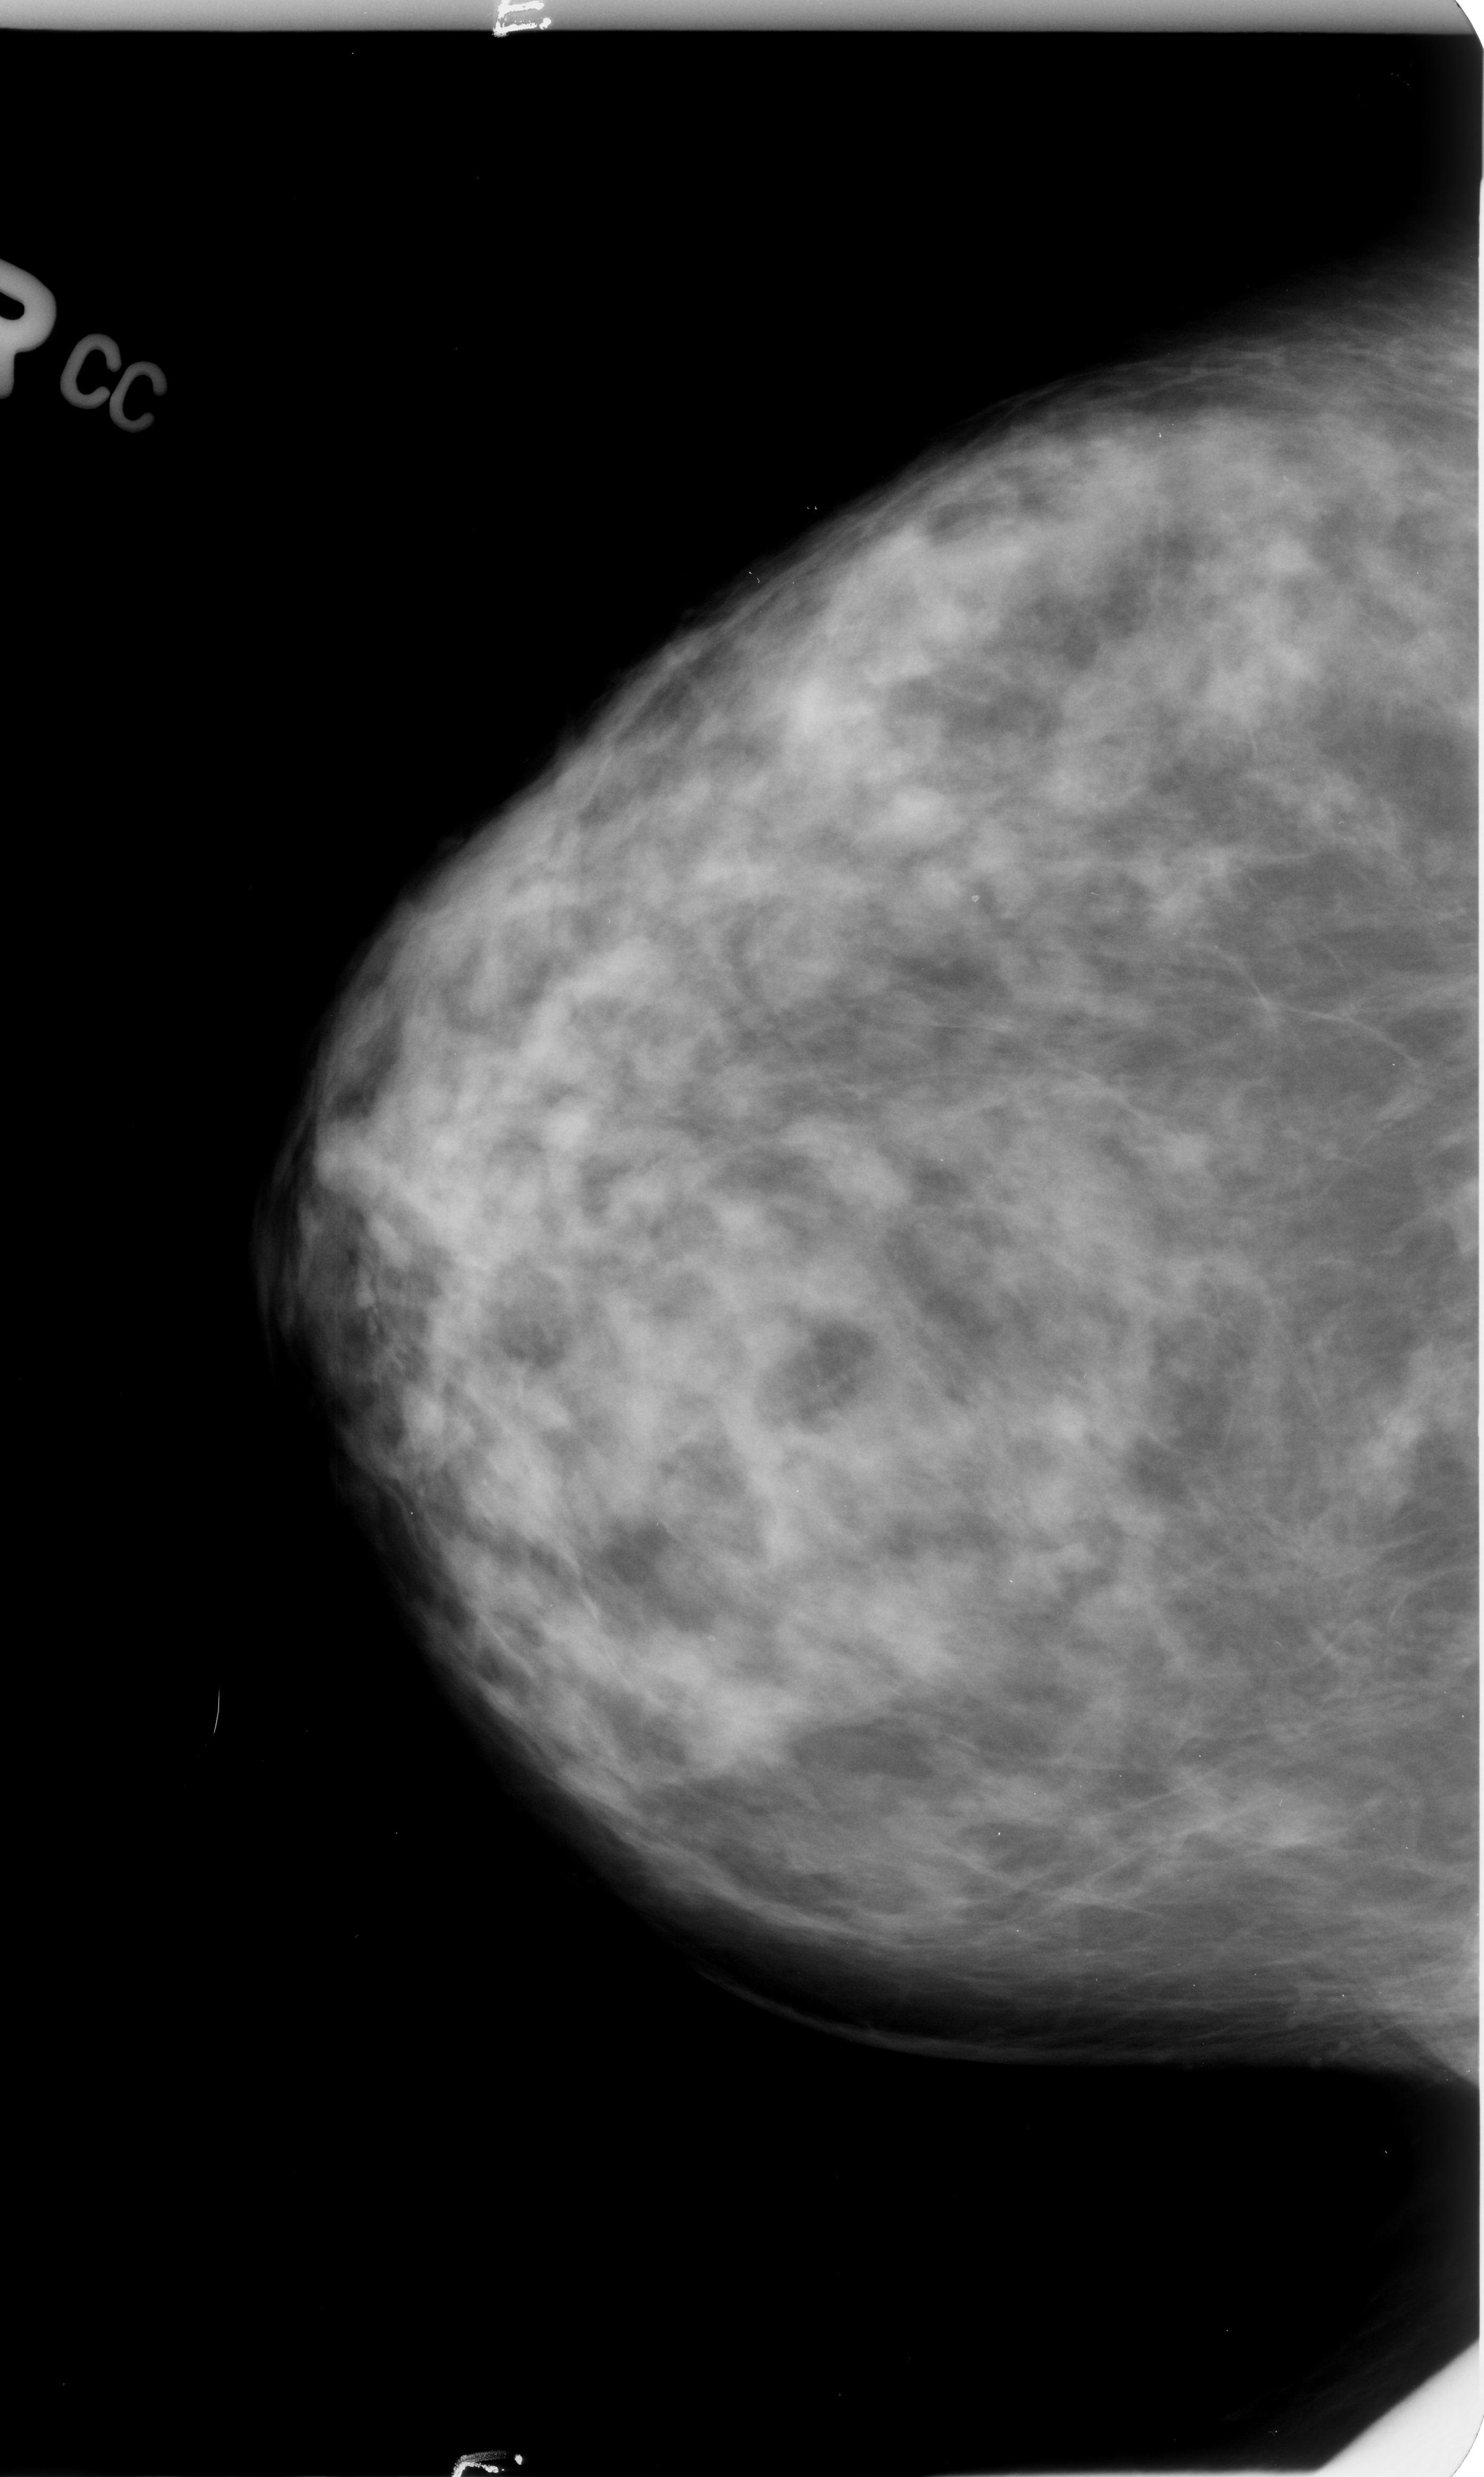
Digitized screen-film mammogram; right breast; CC view; breast composition: heterogeneously dense (BI-RADS density category 3 of 4); 1484 × 2477 image matrix.
Marked abnormalities (boxes around the expert regions of interest):
- calcifications, morphology pleomorphic, distribution clustered; BI-RADS assessment category 4; pathology (as recorded): benign: bounding box (x1, y1, x2, y2) in pixels: (1146, 444, 1434, 651)